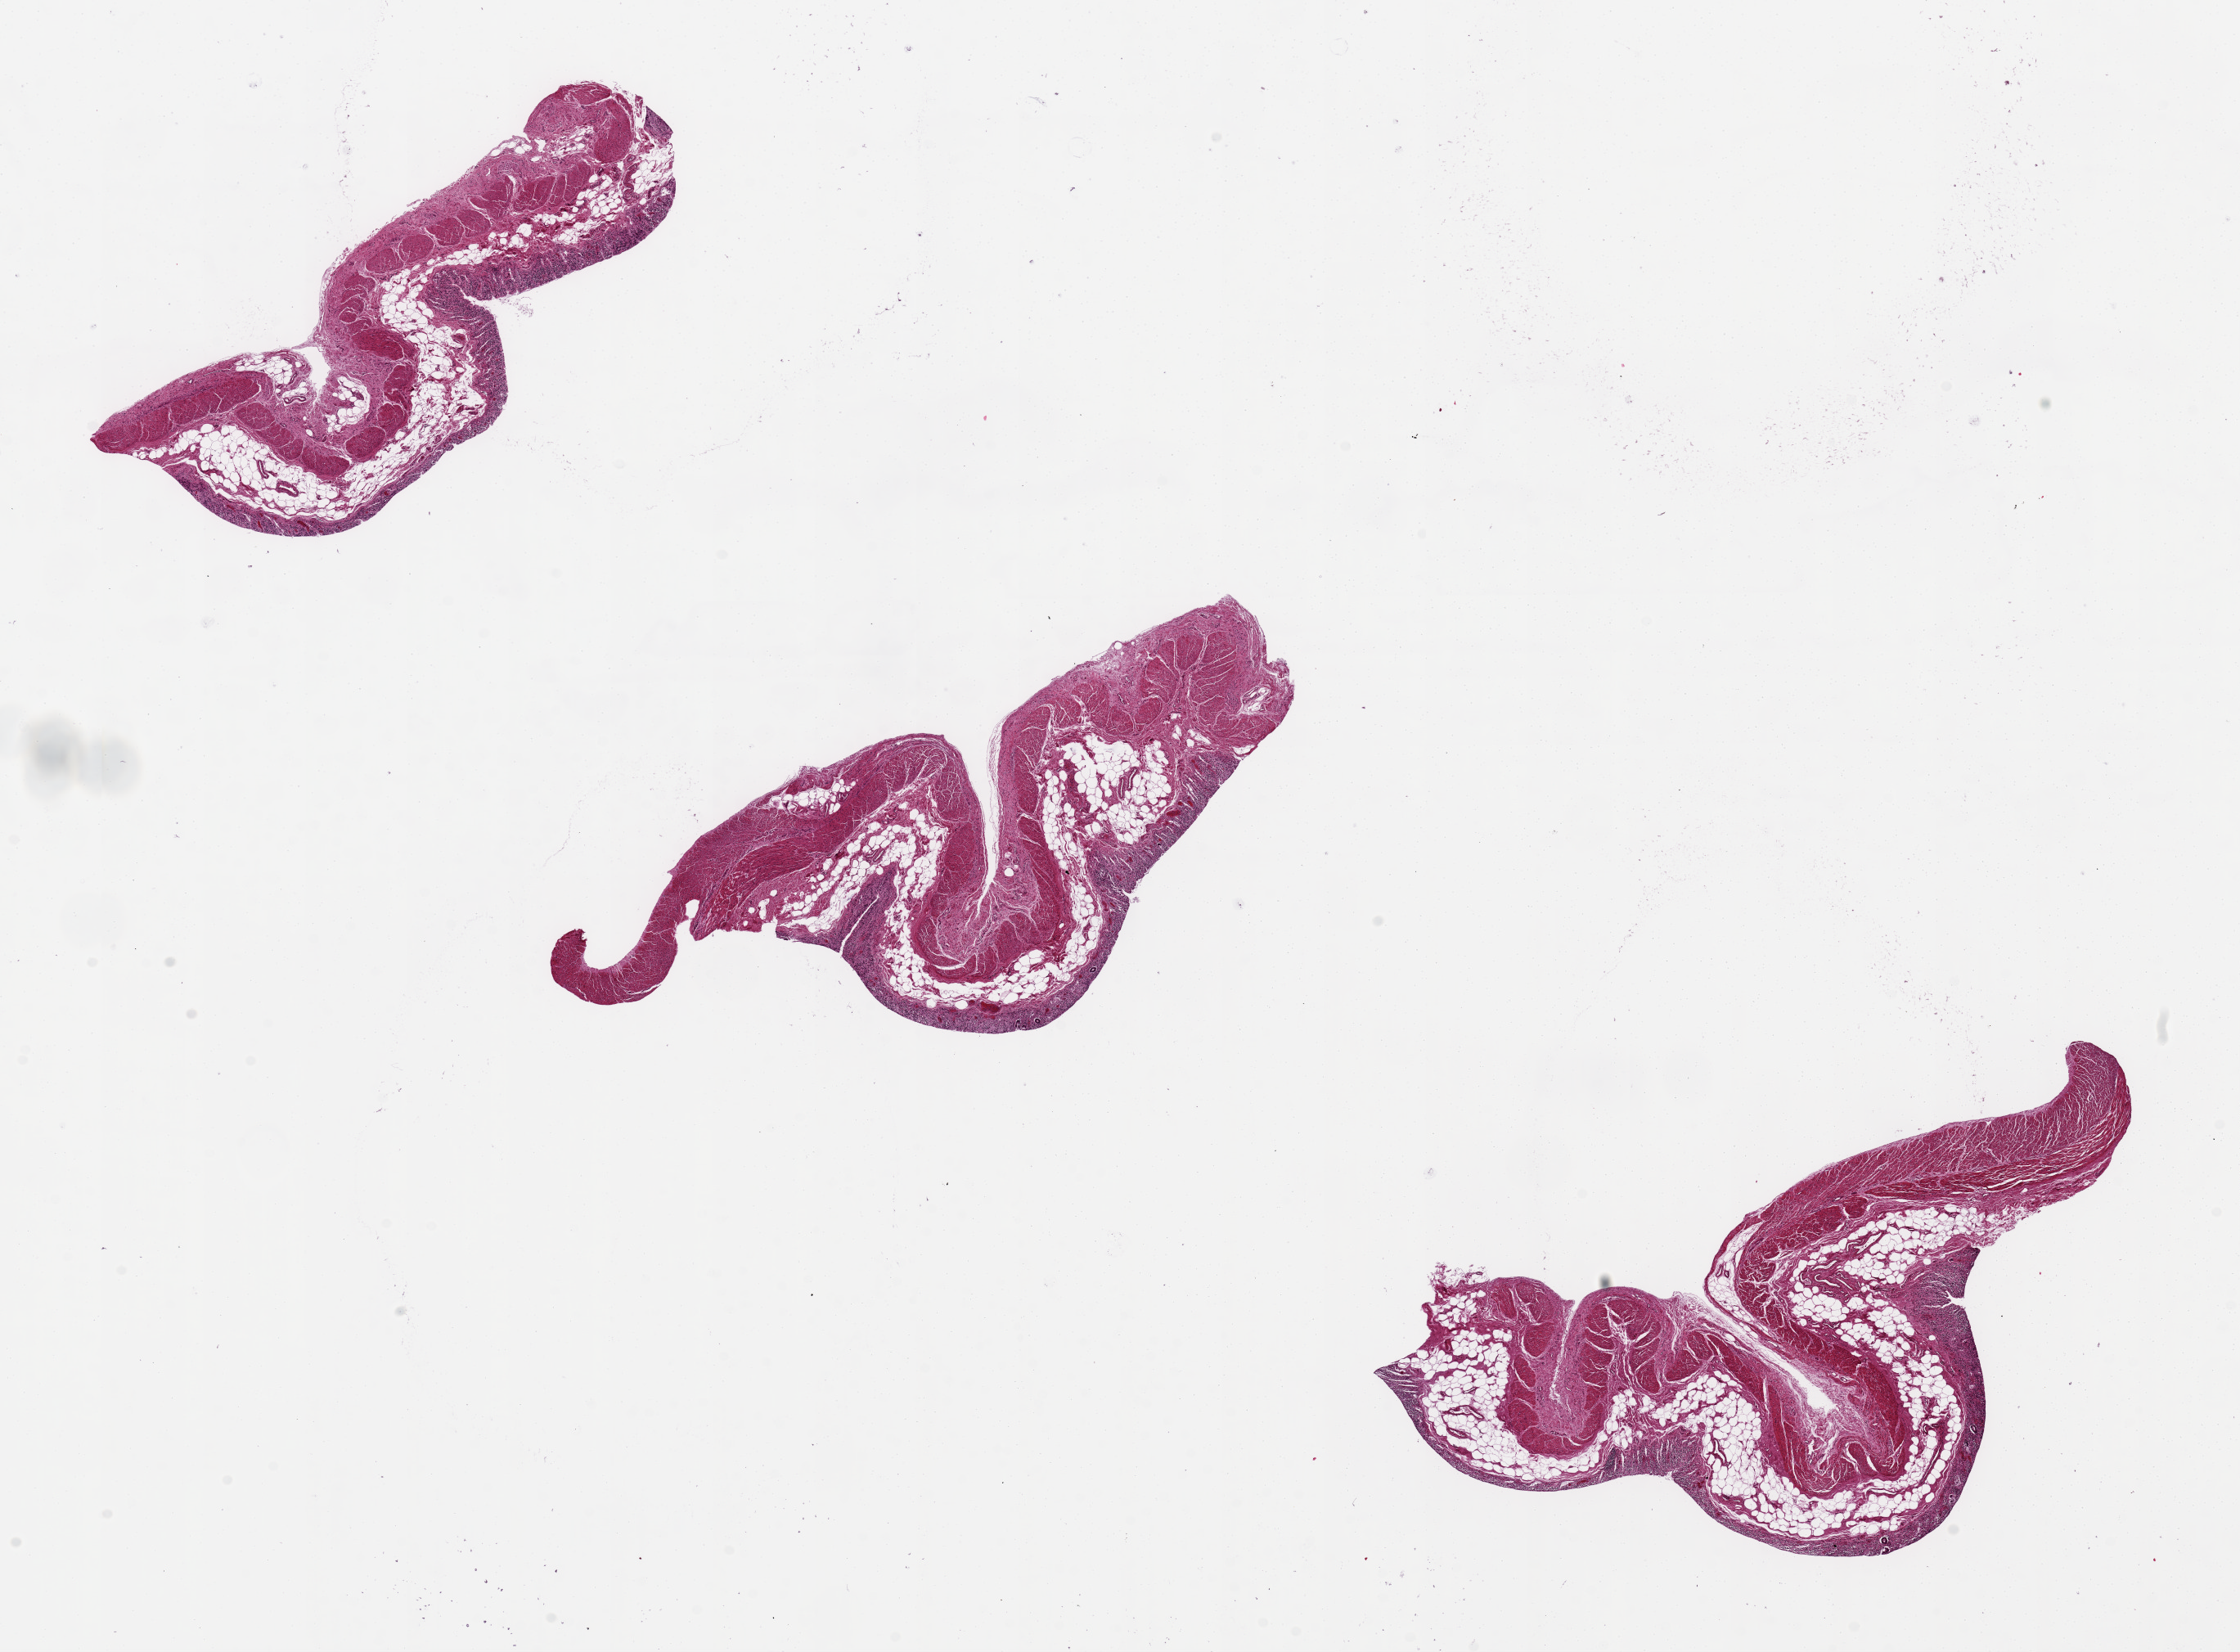
Digitized haematoxylin and eosin-stained section, low-resolution overview of the scanned area, about 21.7 x 16.0 mm (from a 20x scan), PAXgene-fixed, paraffin-embedded tissue, target tissue: transverse colon, tissue donor sample. Male donor.
Review note (as recorded): 3 ~6x4mm pieces. Mucosa totally autolyzed; only a few remnant gland fragments, about 10% of specimen thickness.